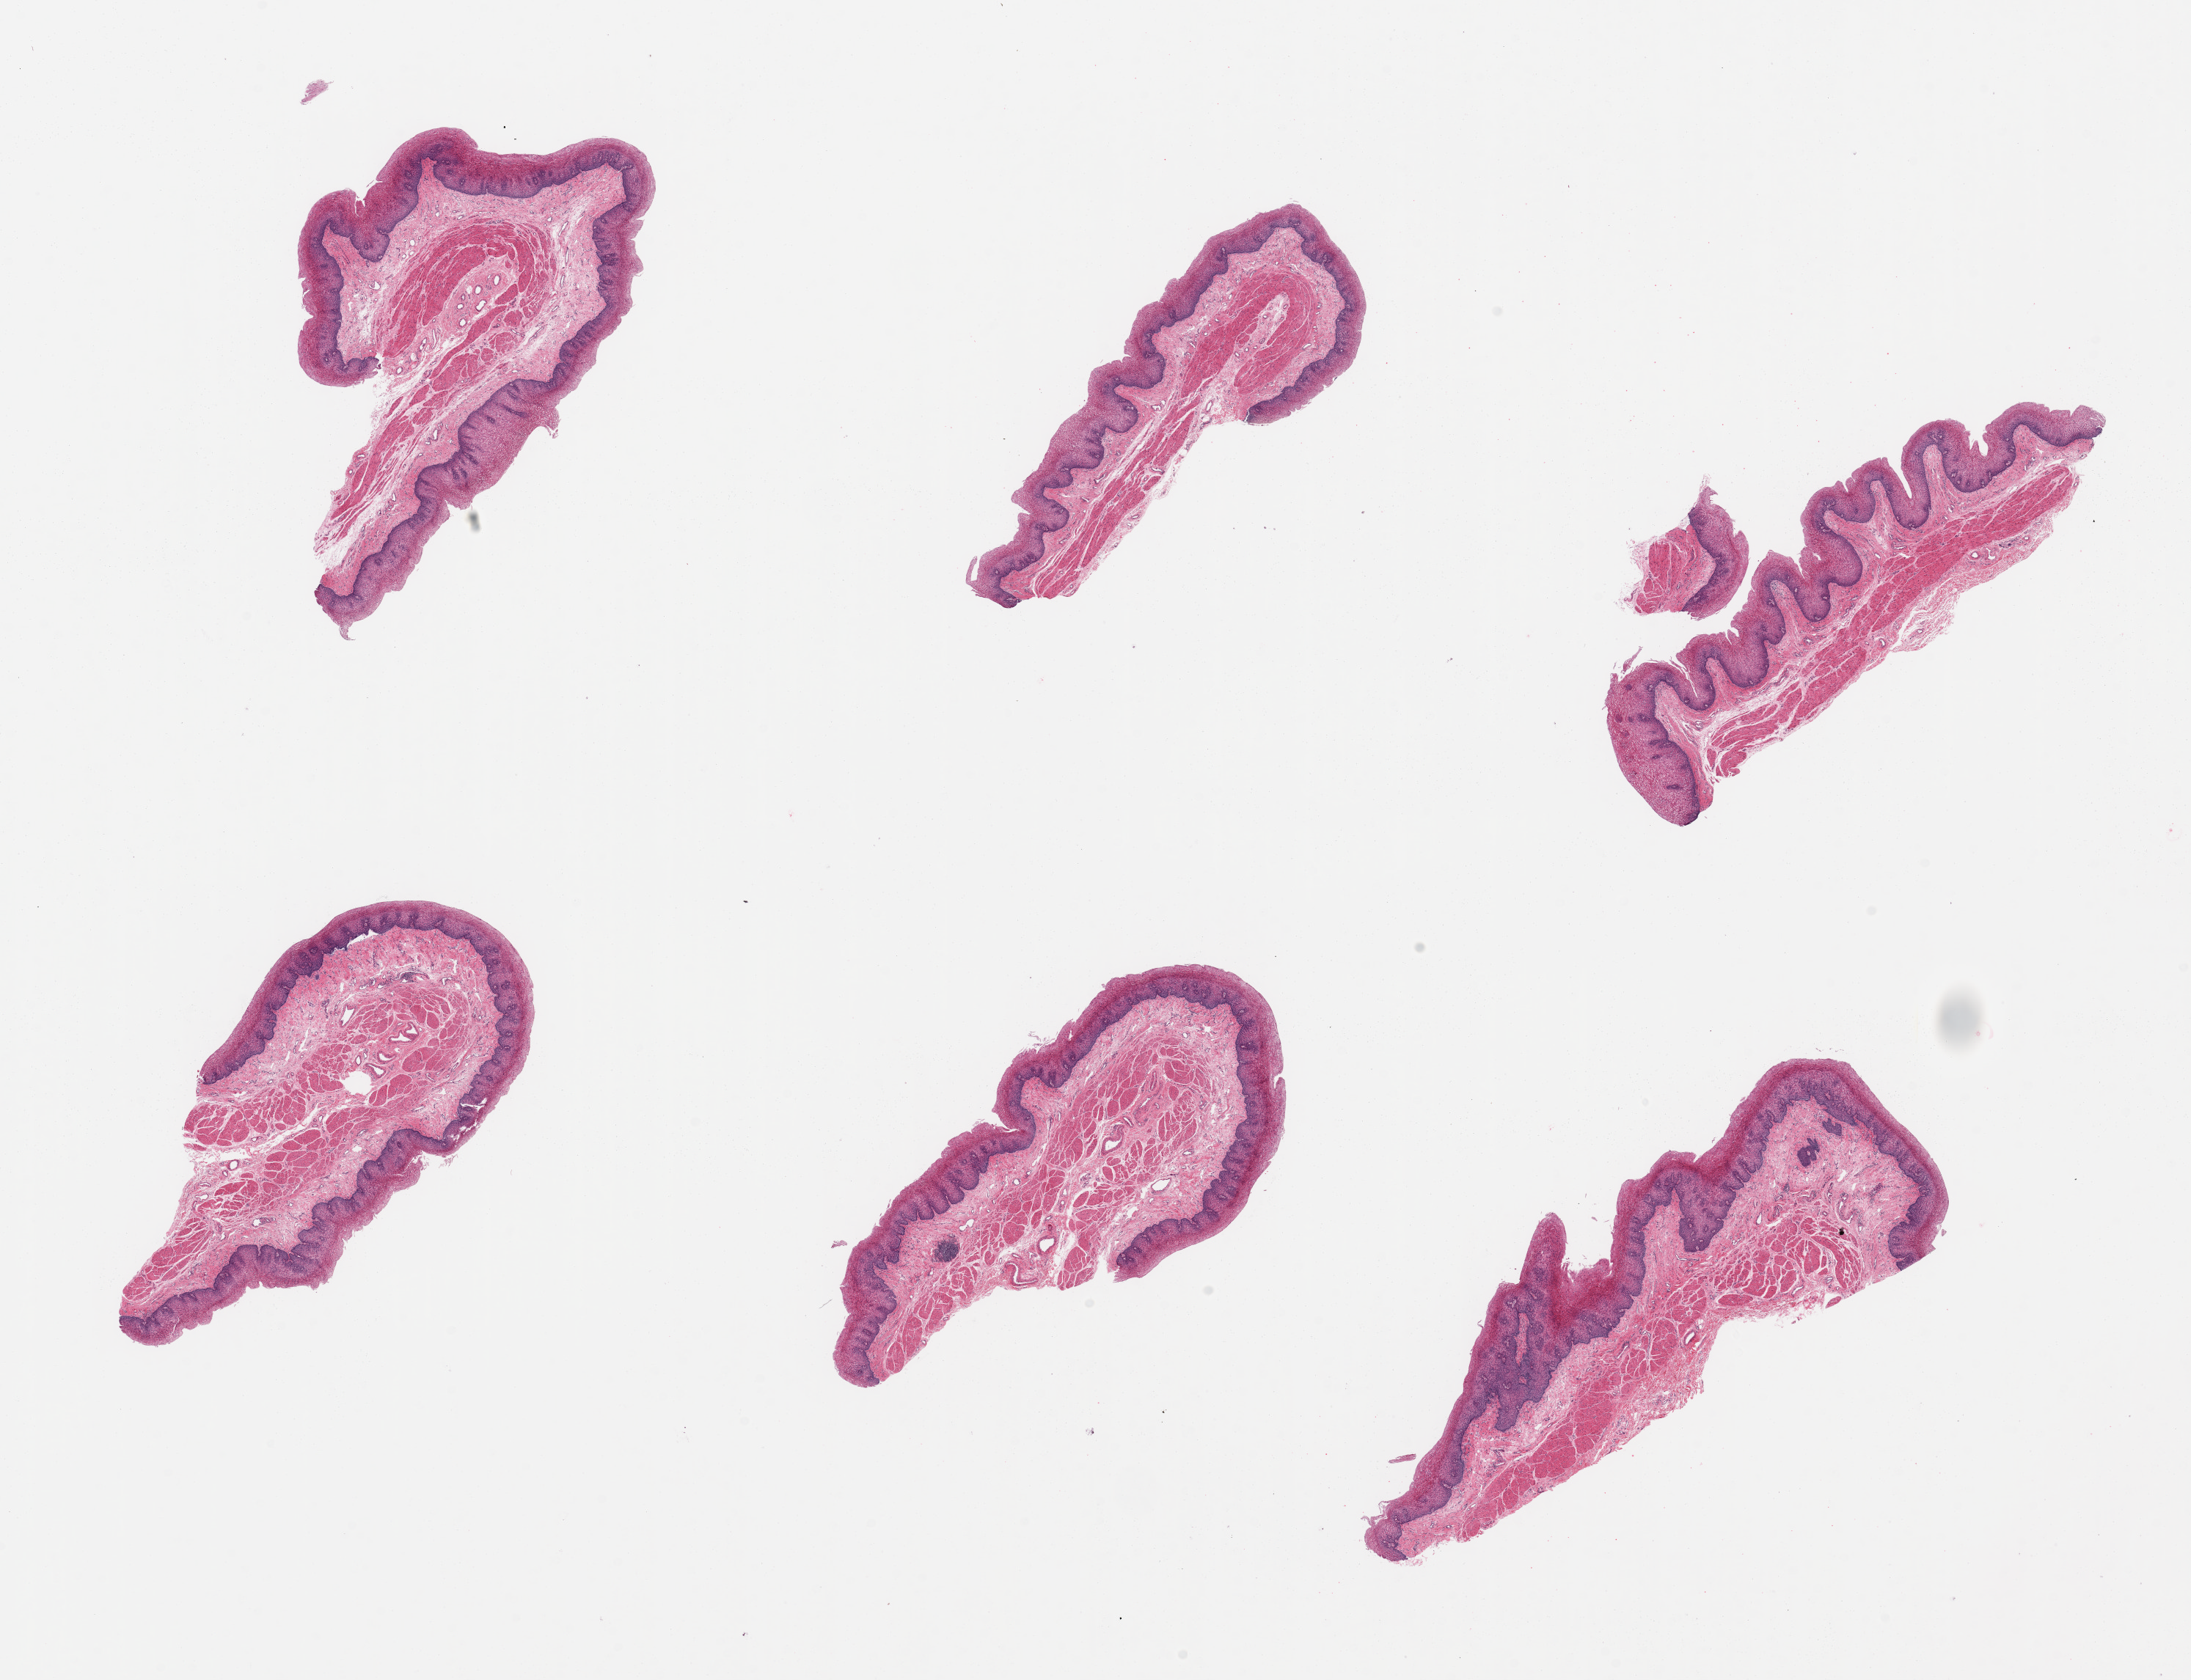
Digitized H&E-stained section — shown as a low-resolution overview of the whole scanned area (about 23.6 x 18.1 mm, acquisition: 20x scan). PAXgene-fixed, paraffin-embedded tissue. Sampled site (target tissue): esophageal mucous membrane. Tissue donor sample. Donor: male.
- pathologist's review note for this sample: 6 pieces; slightly hyperplastic squamous layer